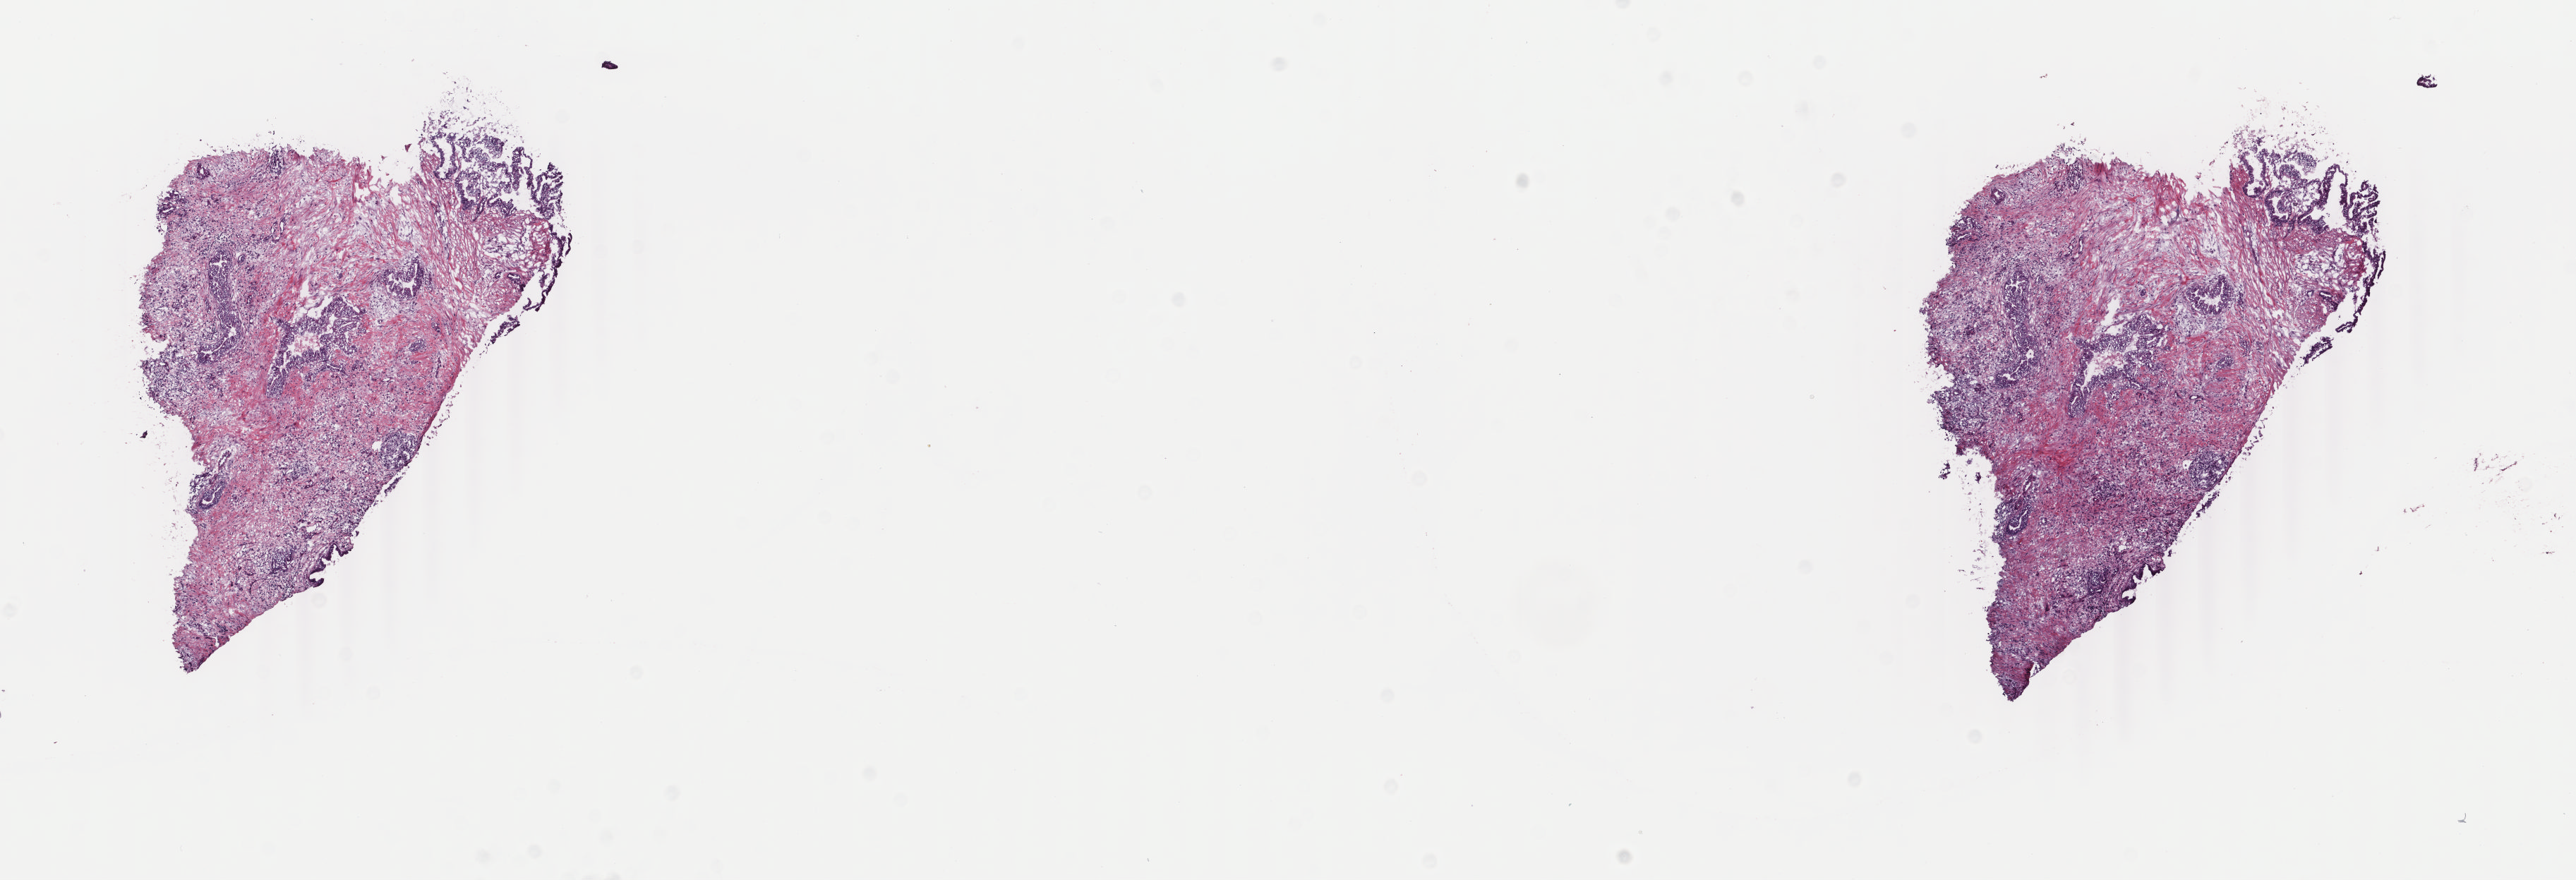
Whole-slide histology image, H&E-stained, a low-resolution overview of the entire scanned area, about 14.5 x 5.0 mm, frozen section, primary tumour sample from the pancreas. Female, age 72 years at initial diagnosis. Histologic grade: G2 (moderately differentiated). Composition of this section per pathologist review: tumour cells 25%, tumour nuclei 80%, normal cells 0%, stromal cells 75%, necrosis 0%. Infiltration values recorded for this section: lymphocyte infiltration 4%, monocyte infiltration 4%, neutrophil infiltration 0%.
AJCC pathologic stage: IIA (7th edition). TNM: T3 N0 MX. Lymph nodes positive (case pathology): 1 of 18 examined. Diagnosis: Infiltrating duct carcinoma, NOS (tail of pancreas).